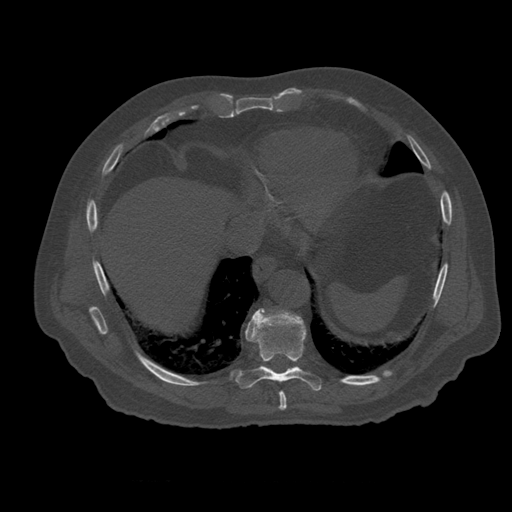
CT including the spine, one axial slice; position 322 of 399 along the scan axis; 120 kVp; bone window (W 1800 / L 400 HU); 1.25 mm slice thickness; 512 × 512 image matrix, field of view 407 × 407 mm. Patient age 73 years. From the clinical record (not read from this slice): primary cancer: prostate; vertebrae with lytic lesions (as recorded): L2.
Structures marked on this image (semi-automatically segmented with operator editing):
- T8 vertebra: bounding box <279,392,287,411> (left, top, right, bottom; pixels)
- T9 vertebra: <235,308,322,391>